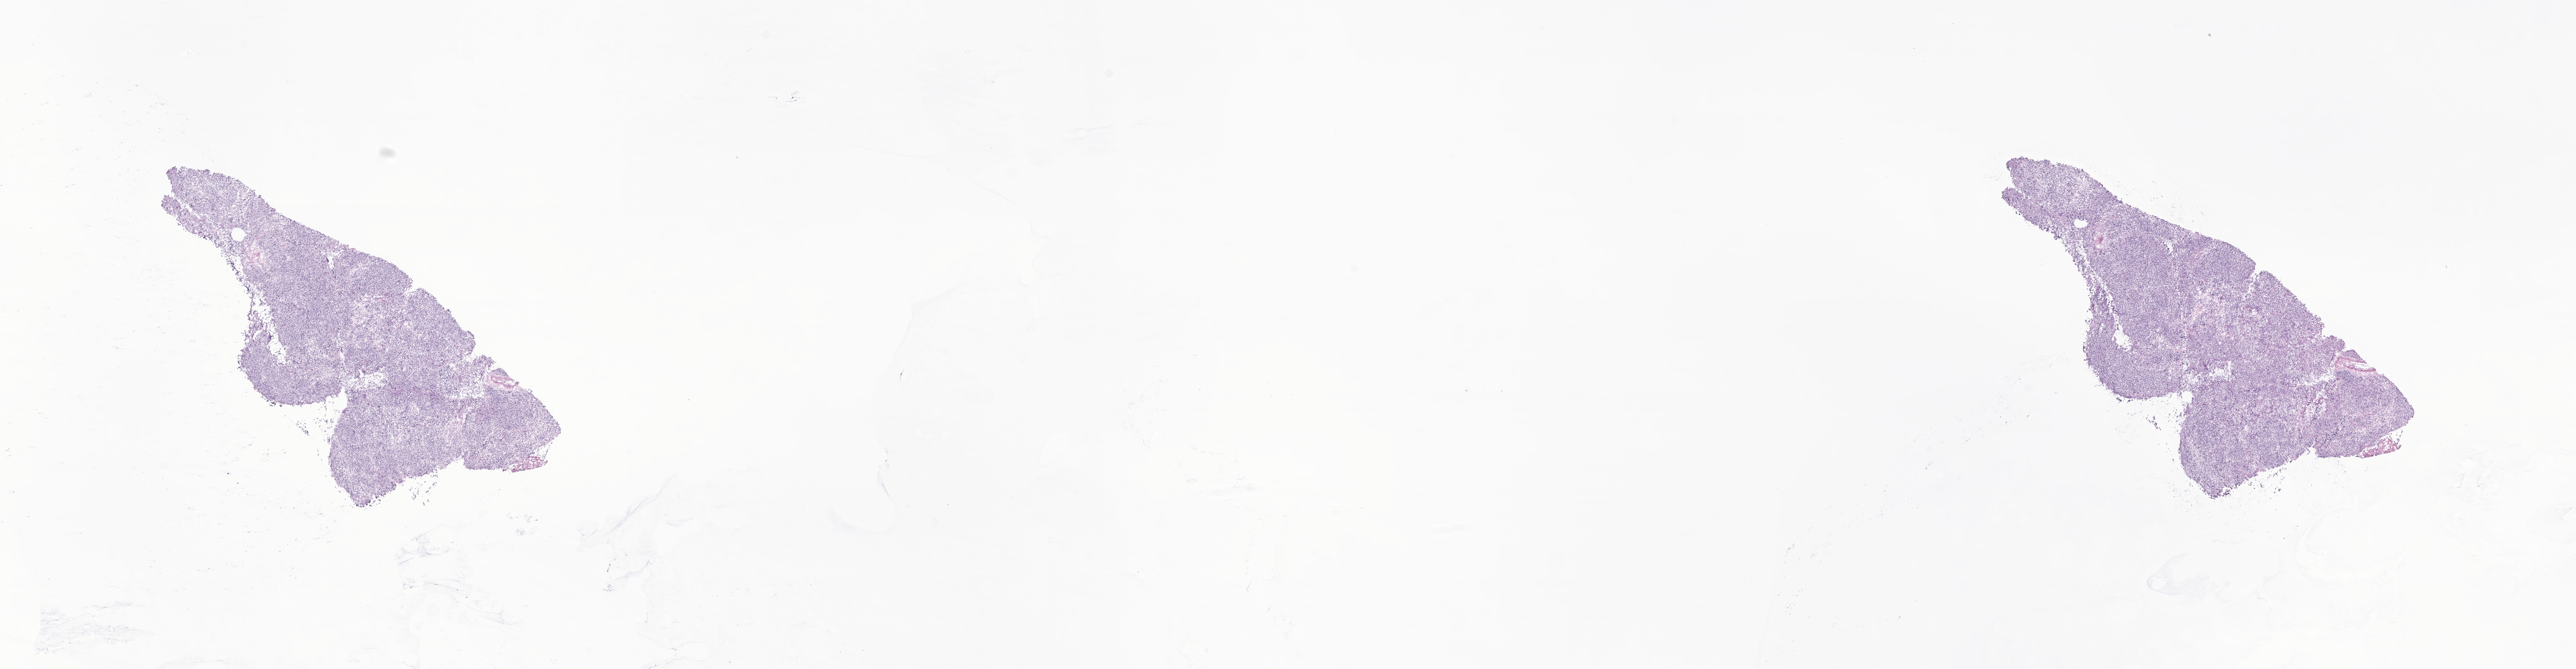
Digitized haematoxylin and eosin-stained section of tumor tissue from the abdomen — a low-resolution overview of the entire scanned area, about 29.6 x 7.7 mm; frozen section. Patient: male, age 129 days.
* diagnosis (ICD-O-3 morphology term): Neuroblastoma, NOS